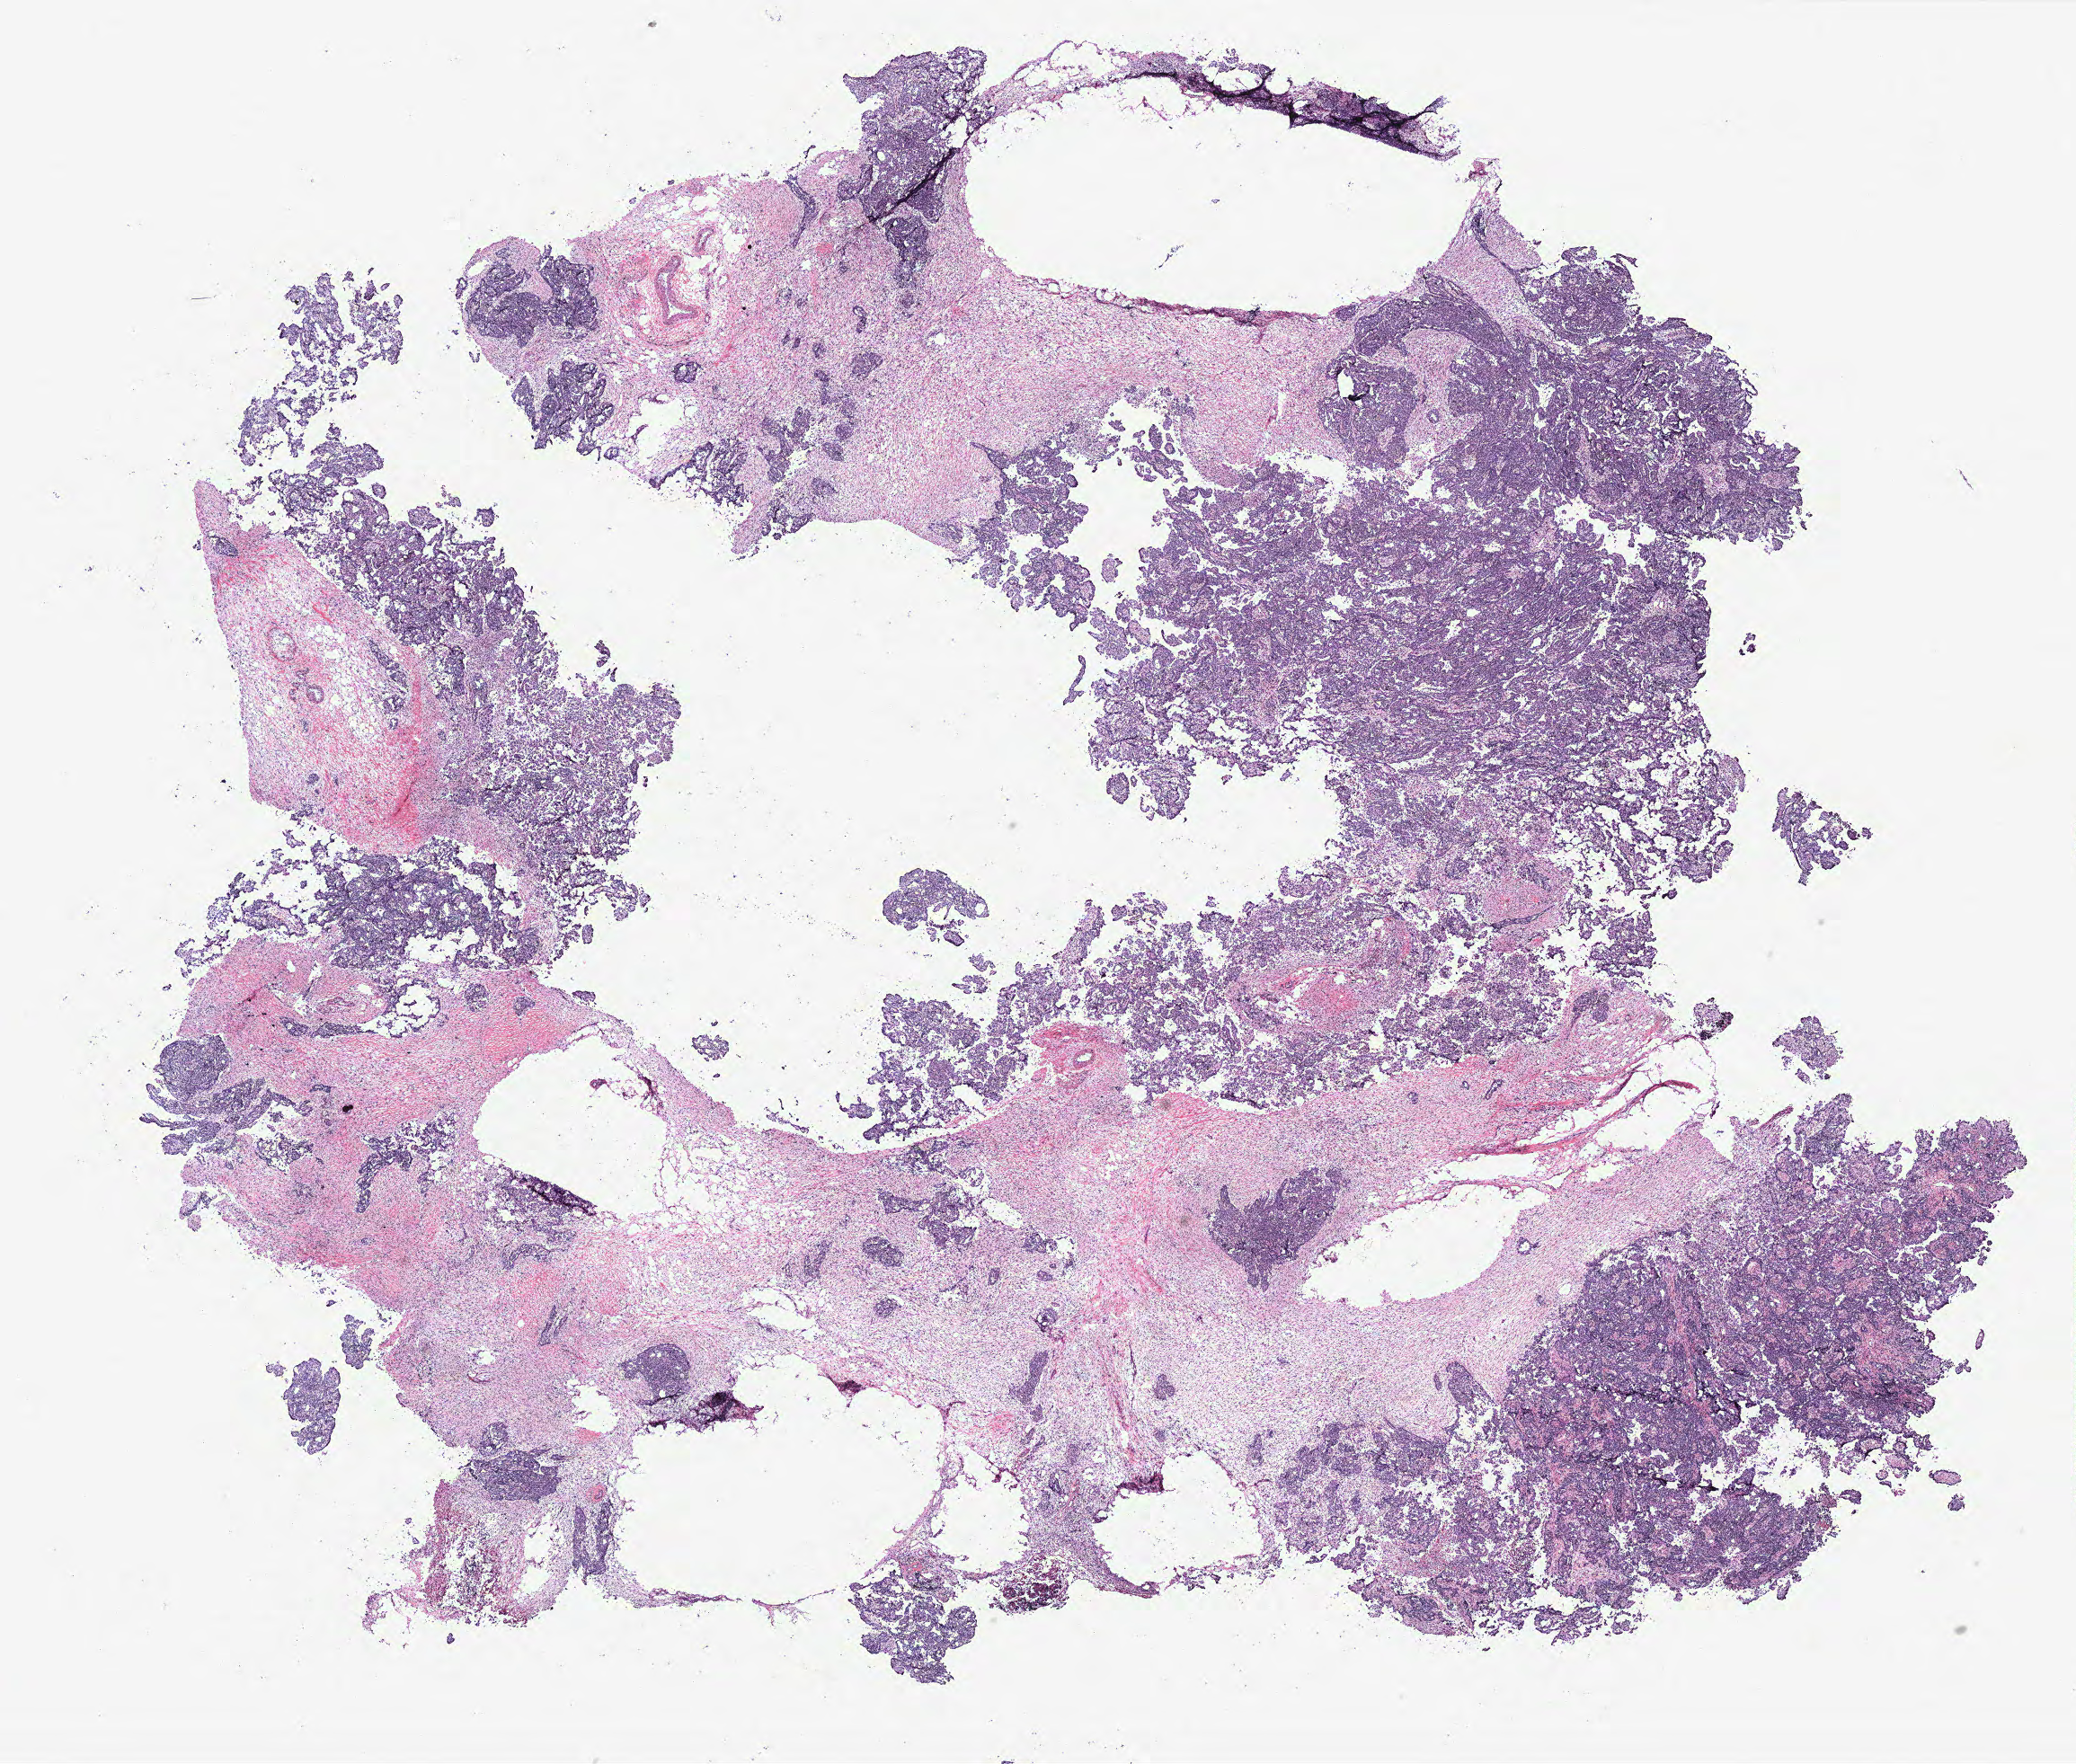
Whole-slide histology image, H&E, low-resolution overview of the scanned area, about 18.5 x 15.7 mm (from a 40x scan); tumour tissue sample, ovary. Patient: female, age 59 years.
• primary tumour site (as recorded): fallopian tube
• diagnosis: Serous adenocarcinoma, NOS (fallopian tube)